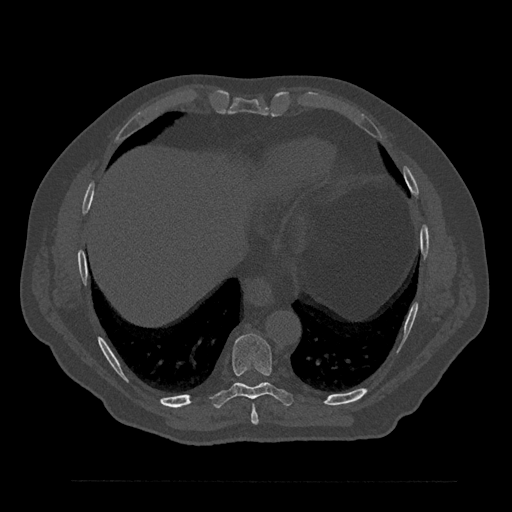
CT including the spine, one axial slice. Slice 406 of 797 in the series (ordered by position). Bone window (W 1800 / L 400 HU). 512 × 512 image matrix. Patient: male, 61 years. From the clinical record (not read from this slice): primary cancer: prostate.
Outlined on this slice (semi-automatically segmented with operator editing):
- T8 vertebra: box from (x=251, y=405) to (x=259, y=425) px
- T9 vertebra: (x=210, y=333)–(x=294, y=408)